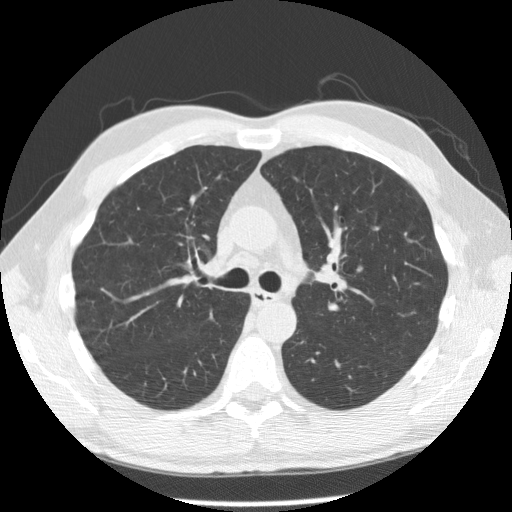
Low-dose screening chest CT, axial slice, second annual screen, lung window (W 1500 / L -600 HU), 512 × 512 image matrix. Male, age 55 years at enrolment. Current smoker at enrolment.
- Expert reader's lesion annotation, box from (x=333, y=248) to (x=374, y=293) px.
- Screening reader's record for this exam: no non-calcified nodule ≥4 mm recorded.
- Later outcome: lung cancer diagnosed 356 days after this screen (after the third annual screen) — small cell carcinoma, NOS, left upper lobe, undifferentiated (G4), stage IV (AJCC 6th edition), 60 mm at pathology.